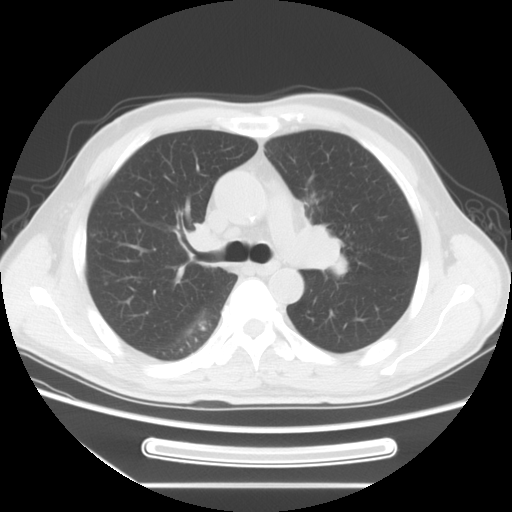
Chest CT, one axial slice. Slice 47 of 71 in the series (ordered by position). Reconstruction kernel STANDARD. 120 kVp. Lung window (W 1500 / L -600 HU). 5 mm slice thickness. 512 × 512 image matrix, field of view 366 × 366 mm. Male patient, age 51 years. From the clinical record (not read from this slice): clinical TNM (as recorded): T1c N3 M0.
Annotated regions visible in this slice (bounding box drawn by a radiologist):
- lung tumour (recorded histology: adenocarcinoma): bounding box <287,203,367,284> (left, top, right, bottom; pixels)